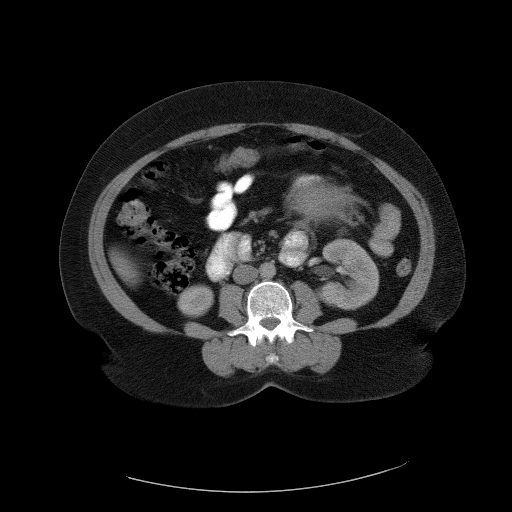
Contrast-enhanced abdominal CT, one axial slice. Slice 51 of 90 in the series (ordered by position). 120 kVp. Intravenous contrast given. Soft-tissue window (W 400 / L 40 HU). 5 mm slice thickness. 512 × 512 image matrix, field of view 480 × 480 mm. Patient: female, 55 years. From the clinical record (not read from this slice): diagnosis: adrenocortical carcinoma; tumour side: left adrenal; tumour size at pathology: 22 cm; Ki-67 index: 10 %; stage (as recorded): 3.
Outlined on this slice (semi-automatically segmented with operator editing):
- mass: bounding box <288,183,357,226> (left, top, right, bottom; pixels)